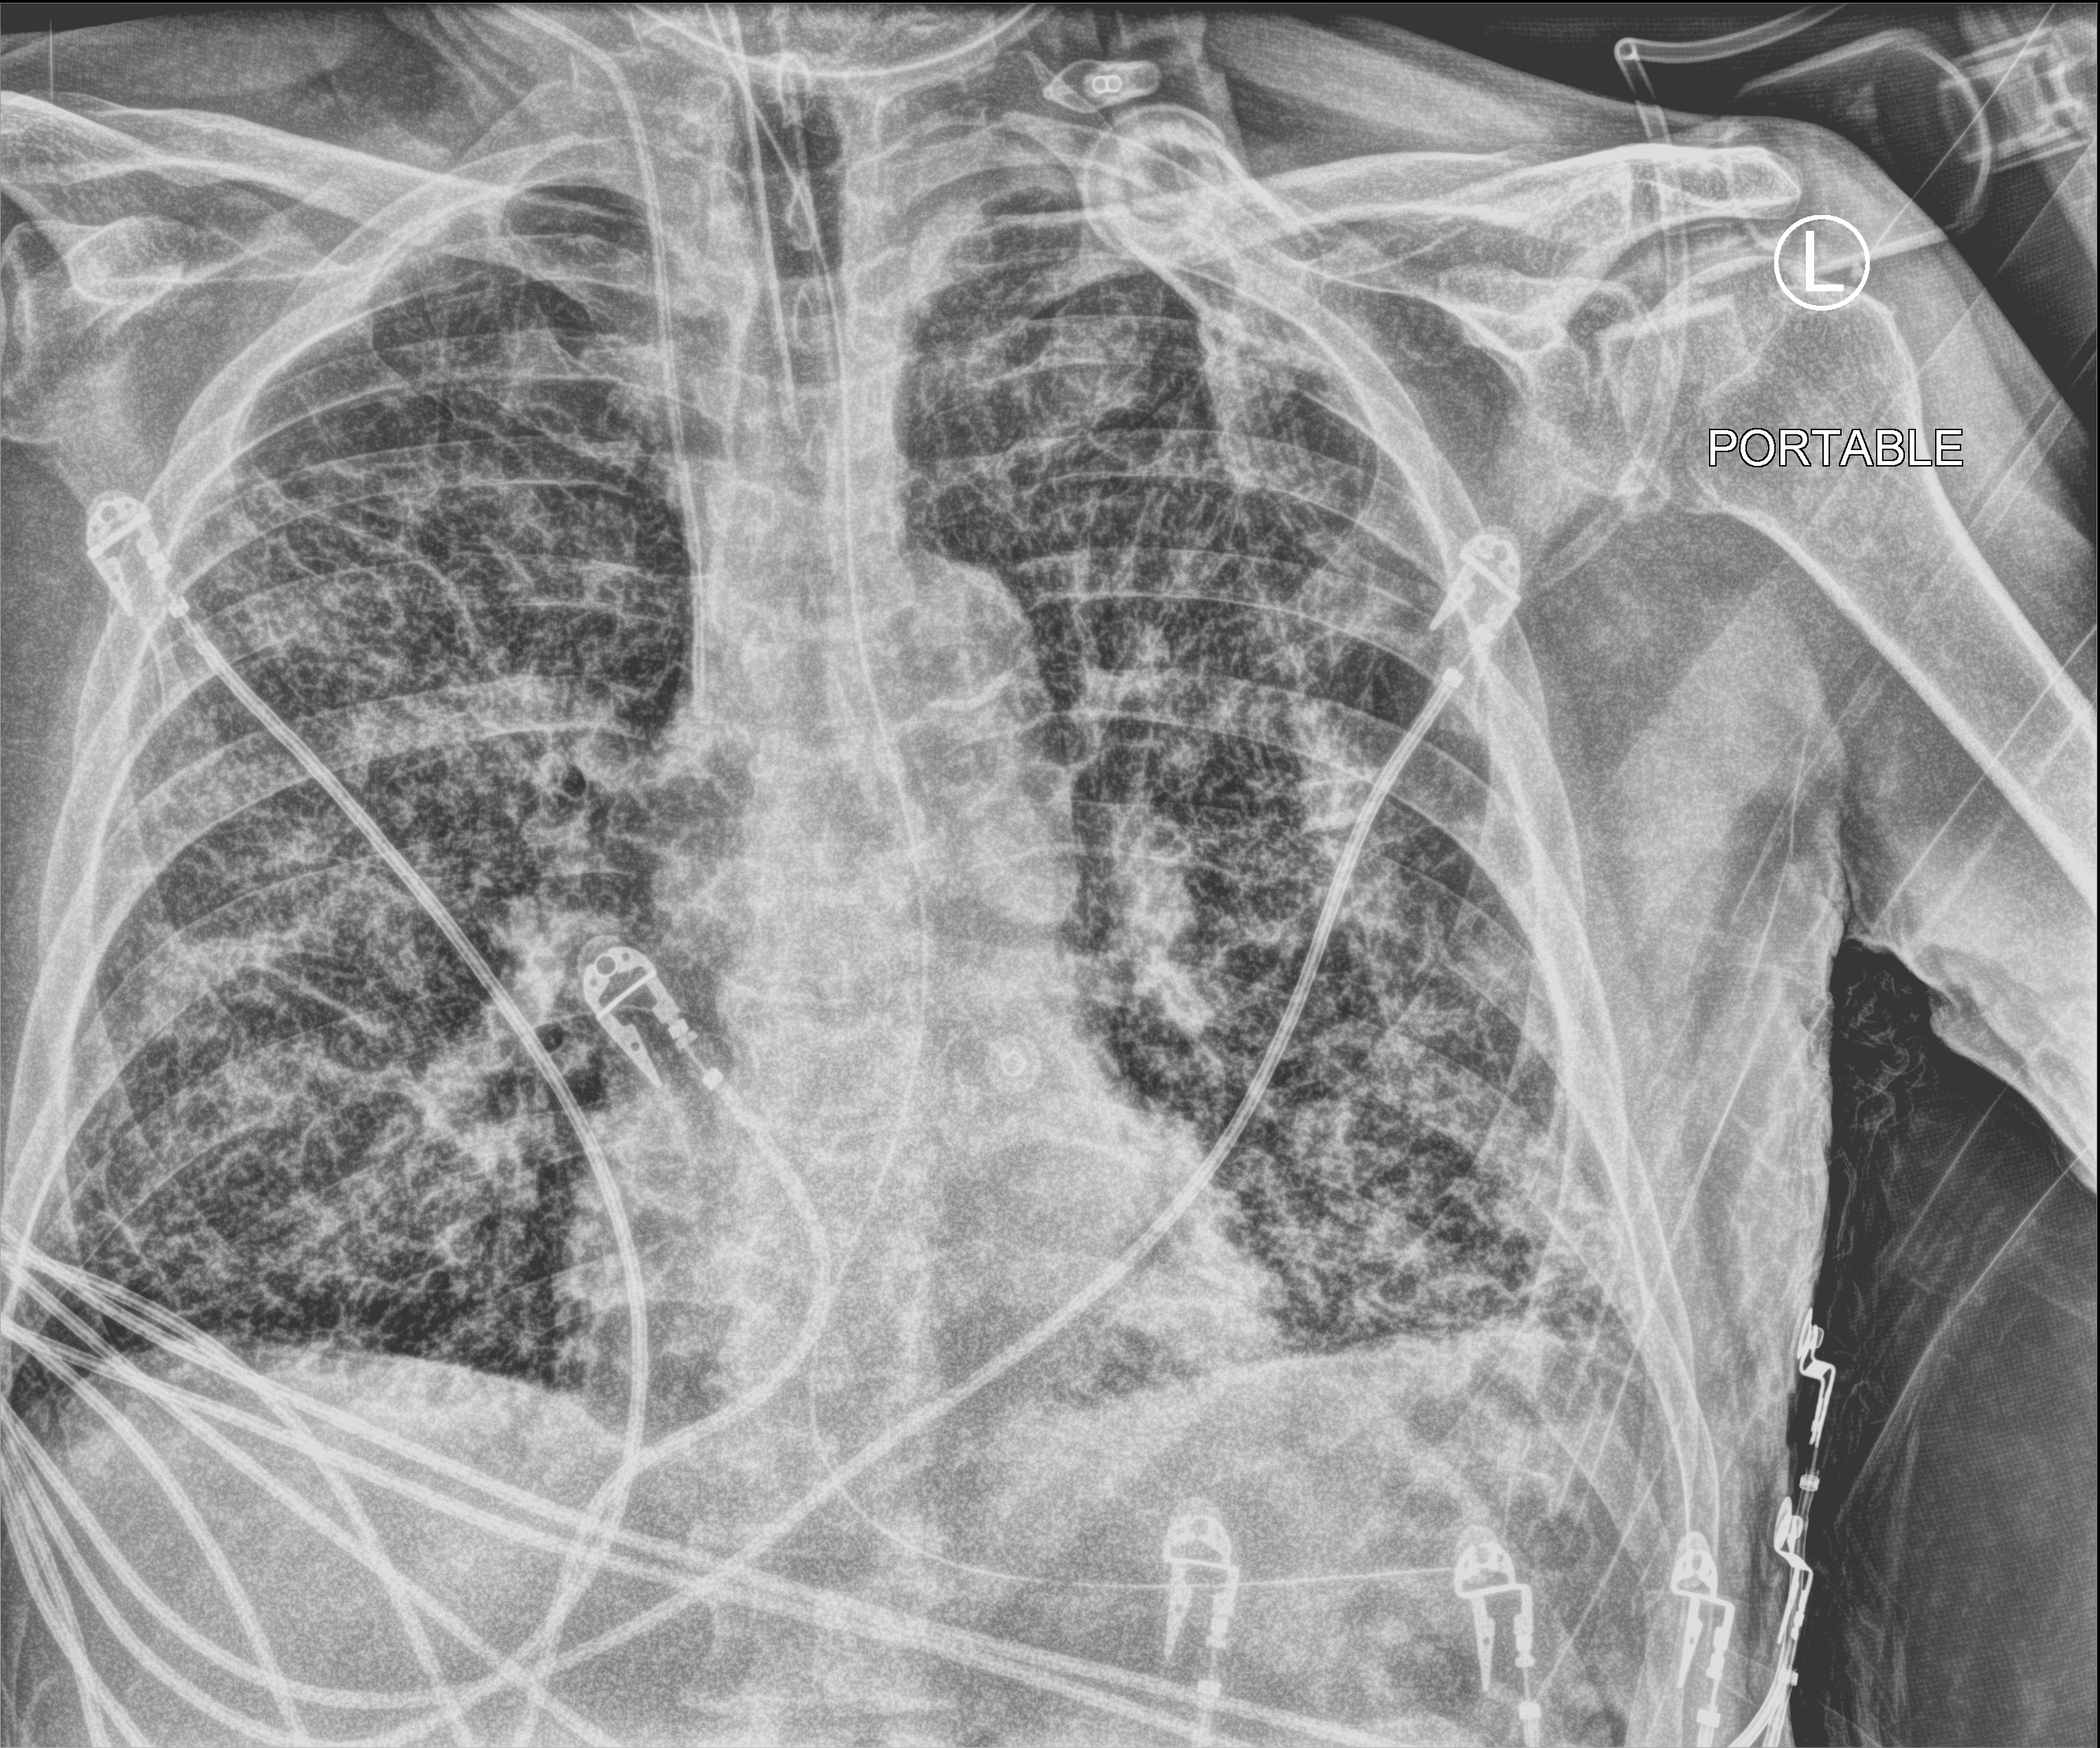
Chest X-ray (portable), anteroposterior (AP) projection. Male patient hospitalised with COVID-19, age 75–90 years.
From the hospital-stay record, not from the radiograph (when in the stay this image was taken is not recorded):
- mechanically ventilated during this hospital stay: yes
- chronic kidney disease (admission record): no
- admitted to intensive care during this hospital stay: yes